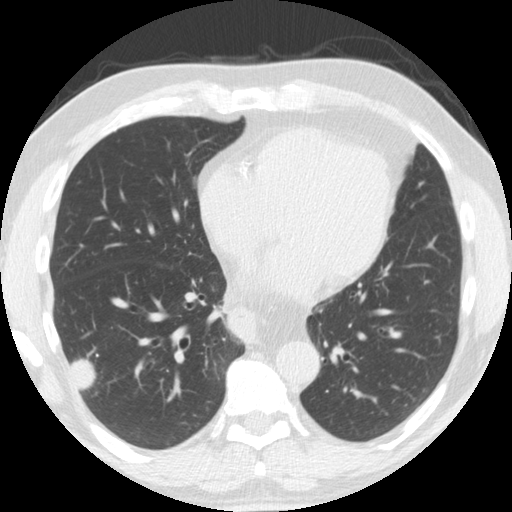
Axial slice from a low-dose chest CT screening exam, second annual screen, lung window (W 1500 / L -600 HU), 2.5 mm slice thickness, 512 × 512 image matrix, field of view 341 × 341 mm. Male, age 61 years at enrolment.
Expert reader's lesion annotation, box from (x=43, y=321) to (x=111, y=398) px. Reader record for this screening exam (exam-level; its link to the box is not recorded): non-calcified nodule or mass ≥4 mm, right lower lobe, 33 × 19 mm, smooth margins, soft tissue attenuation, pre-existing on the prior screen: yes; interval growth: yes. Later outcome: lung cancer diagnosed 30 days after this screen — adenosquamous carcinoma, right lower lobe, poorly differentiated (G3), stage IV (AJCC 6th edition), 45 mm at pathology.